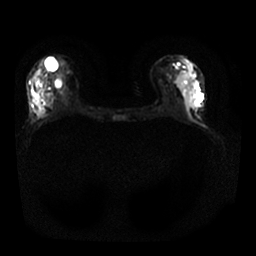
Breast MRI, one axial slice; position 10 of 25 along the scan axis; diffusion-weighted series; image 2 of 4 stored at this slice position (different b-values; order by instance number); 1.5 T; 4 mm slice thickness; 256 × 256 image matrix, field of view 330 × 330 mm. Female patient.
Structures marked on this image (outlined manually by an expert reader):
- tumour on diffusion-weighted imaging: bounding box [x1, y1, x2, y2] px = [36, 98, 44, 118]